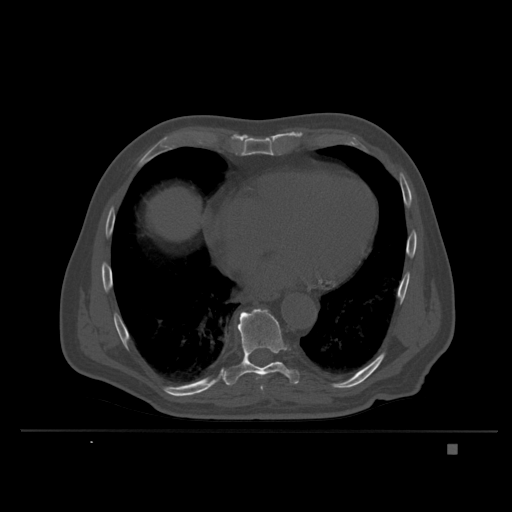
CT including the spine, one axial slice. Position 213 of 435 along the scan axis. Bone window (W 1800 / L 400 HU). 1.5 mm slice thickness. 512 × 512 image matrix, field of view 434 × 434 mm. Male patient, age 73 years. From the clinical record (not read from this slice): primary cancer: skin.
Outlined on this slice (semi-automatic segmentation, software-assisted and operator-edited):
- T9 vertebra: bounding box [x1, y1, x2, y2] px = [223, 308, 300, 394]